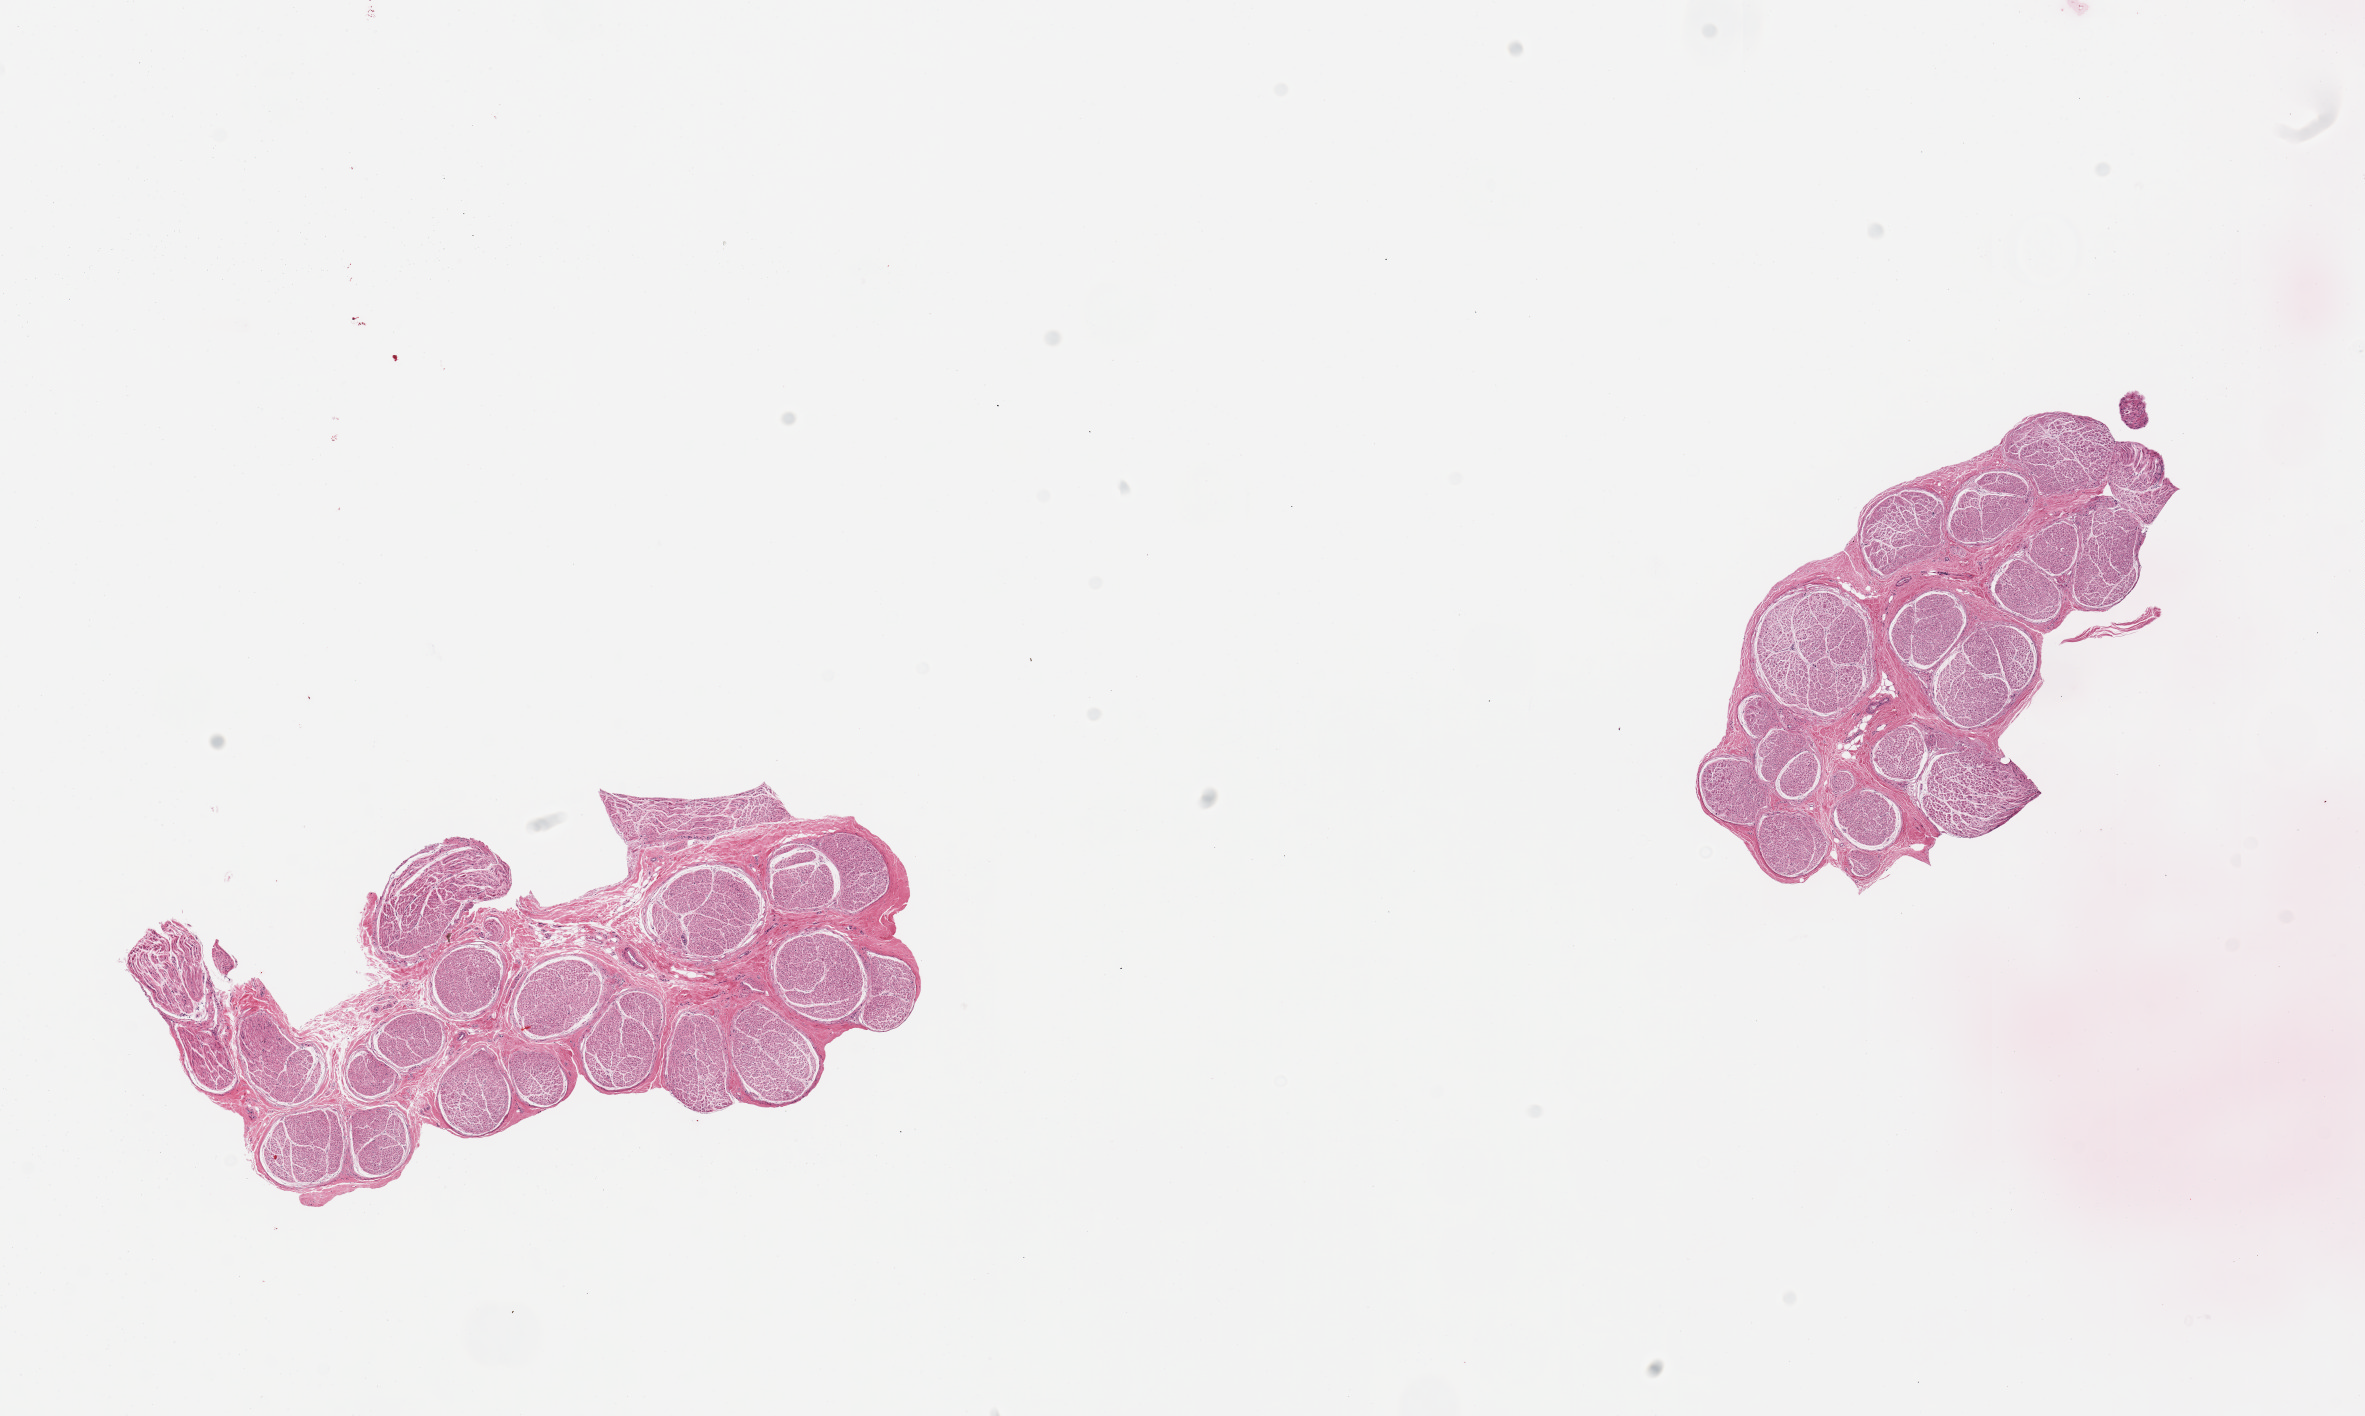
Whole-slide image, hematoxylin and eosin (H&E) stain, whole scanned area (about 18.7 x 11.2 mm) shown as a low-resolution overview. PAXgene-fixed, paraffin-embedded tissue. Target tissue: tibial nerve. Tissue donor sample. Male donor.
Review note (as recorded): 2 pieces, good clean specimens.